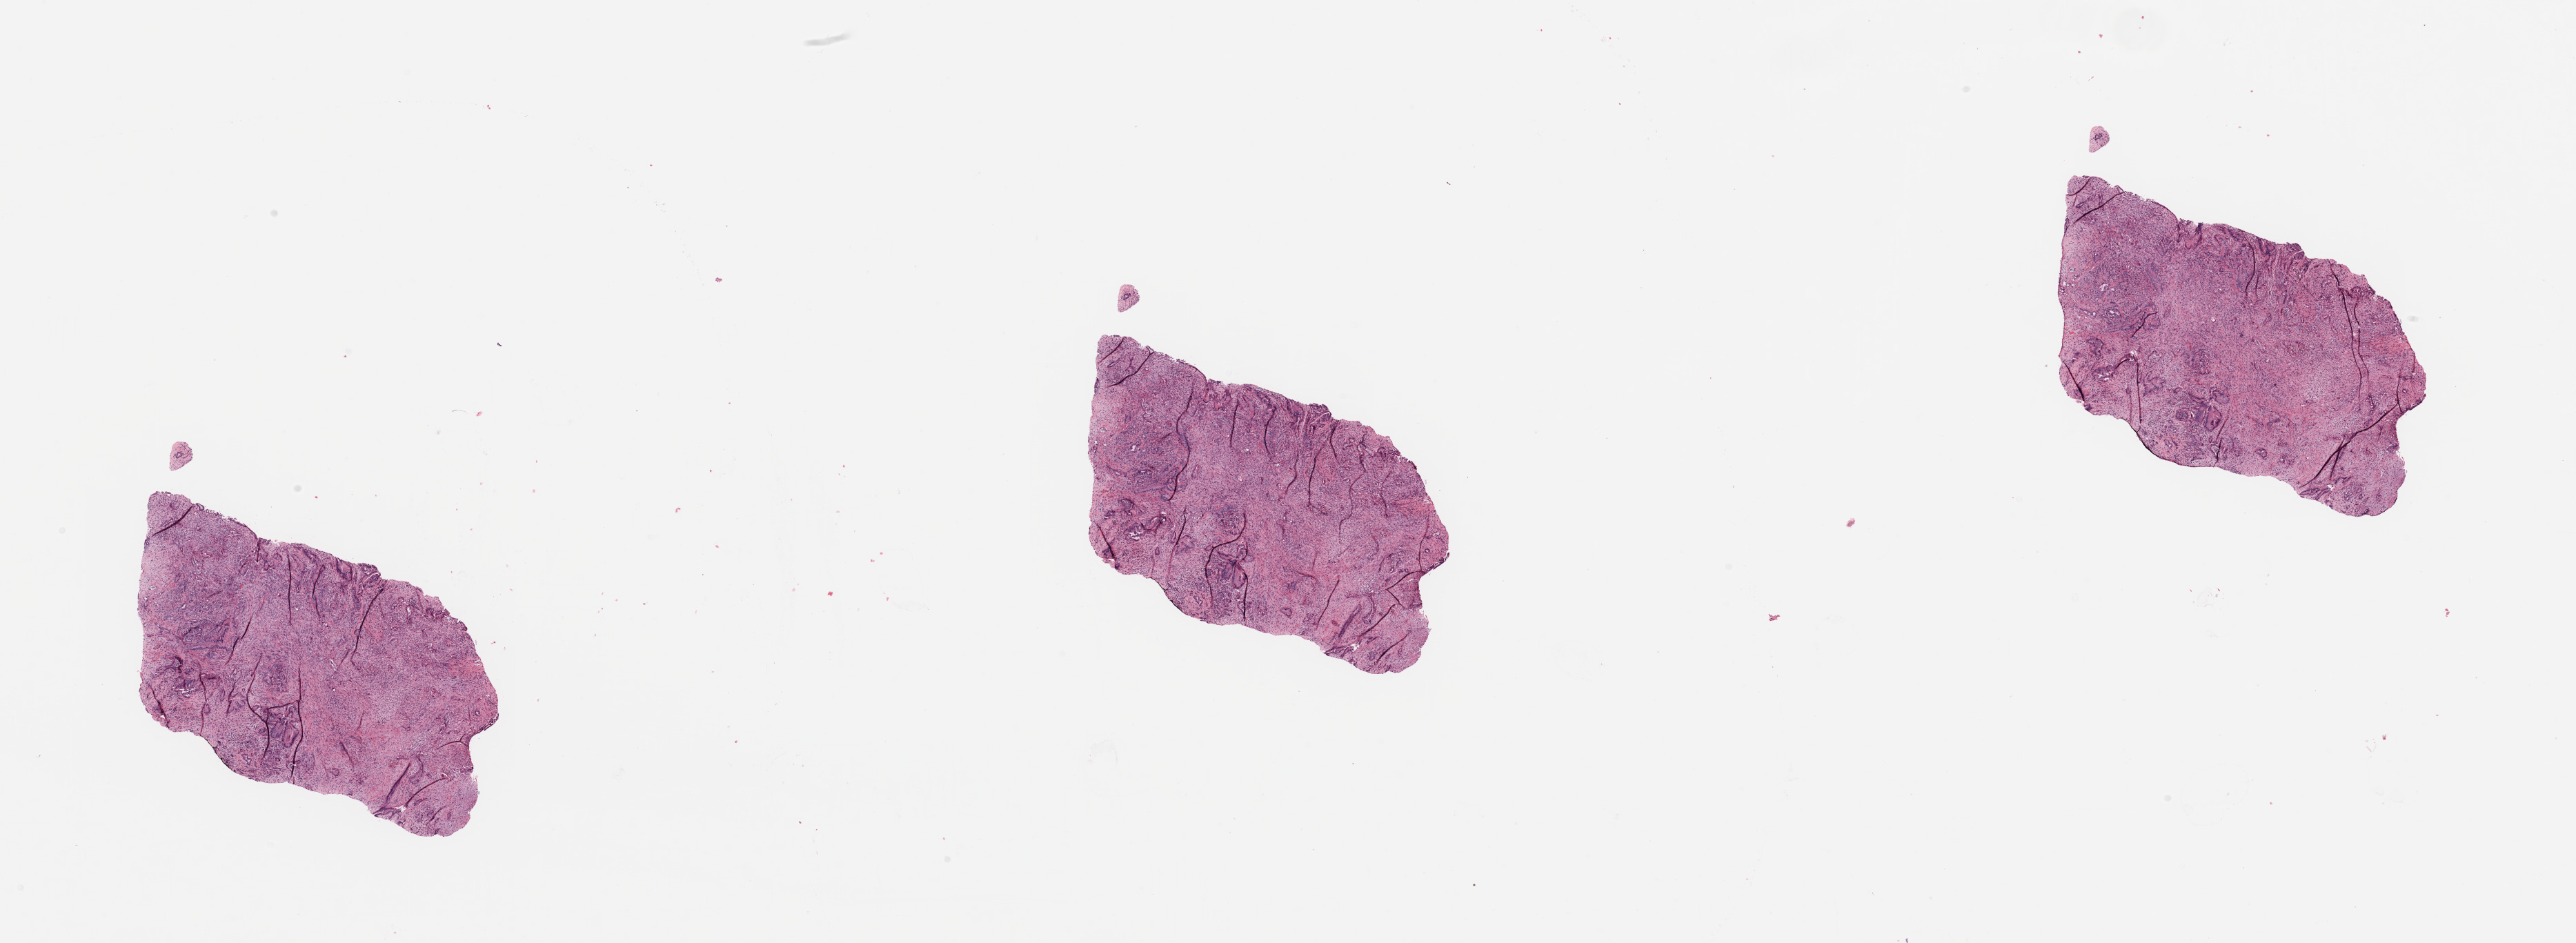
Whole-slide histology image, H&E-stained, whole scanned area (about 29.5 x 10.8 mm, slide scanned at 20x) shown as a low-resolution overview, tumour tissue sample, sampled site: pancreas. Patient: male, age 72 years. Pathologist review of this section (percent, as recorded): tumour nuclei 40%, necrosis 0%.
Diagnosis: Infiltrating duct carcinoma, NOS.